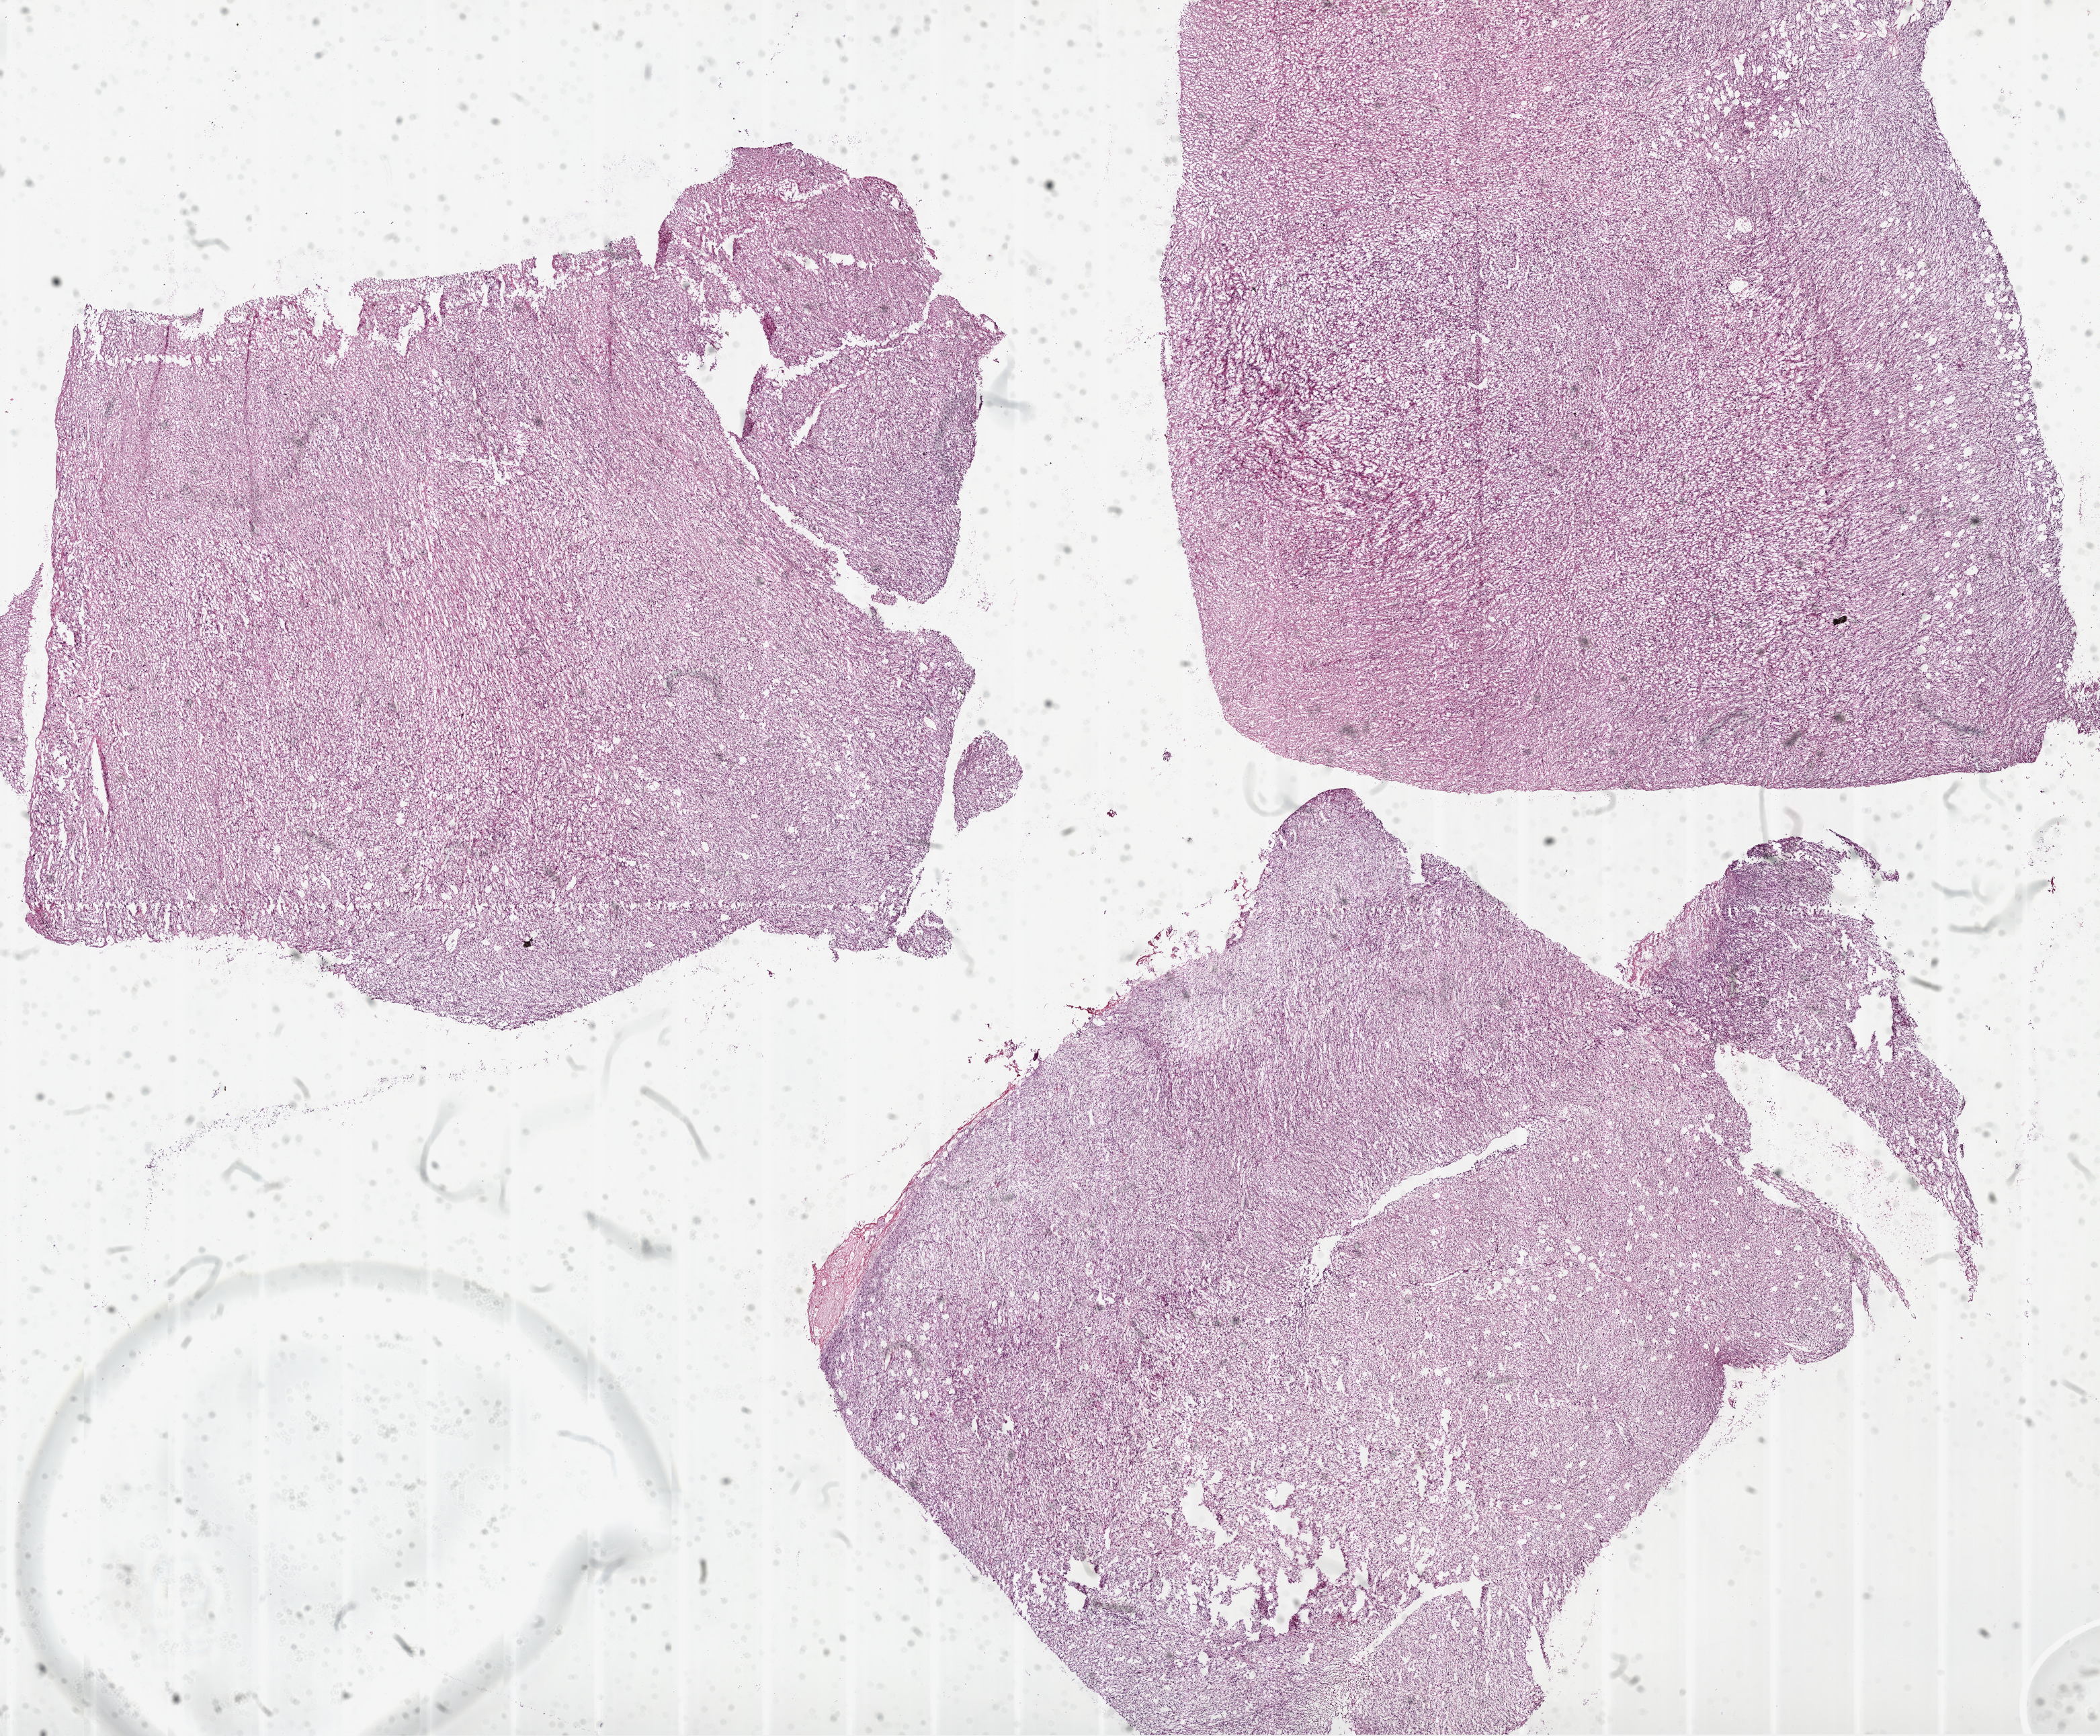
Hematoxylin and eosin (H&E) stained whole-slide image, shown as a low-resolution overview of the whole scanned area (about 25.1 x 20.7 mm, slide scanned at 20x). Frozen section from the bottom of the tissue portion. Sample: primary tumour, kidney. Patient: male, age at initial diagnosis 58 years. Histologic grade: G3 (poorly differentiated). Slide review estimates, as recorded: tumour cells 95%, tumour nuclei 90%, normal cells 0%, stromal cells 5%, necrosis 0%.
- AJCC pathologic stage: III
- diagnosis: Clear cell adenocarcinoma, NOS
- laterality: left